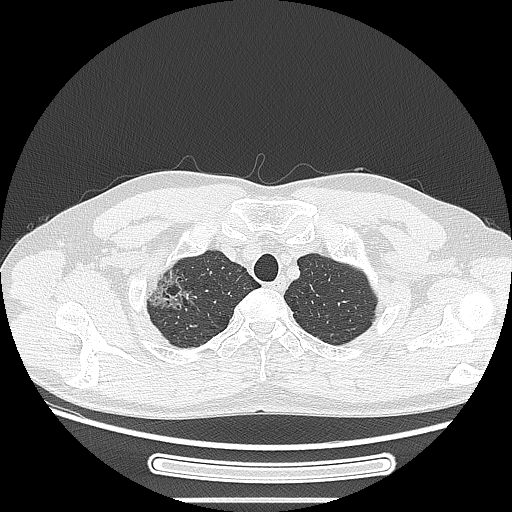
Chest CT, one axial slice; position 232 of 269 along the scan axis; 120 kVp; lung window (W 1500 / L -600 HU); 1.25 mm slice thickness; 512 × 512 image matrix, field of view 382 × 382 mm. Male patient, age 53 years. From the clinical record (not read from this slice): clinical TNM (as recorded): T1c N0 M0.
Outlined on this slice (bounding box drawn by a radiologist):
- lung tumour (recorded histology: adenocarcinoma): bounding box (x1, y1, x2, y2) in pixels: (134, 264, 195, 323)